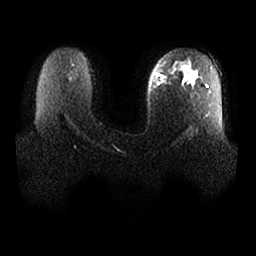
Breast MRI, one axial slice; position 19 of 25 along the scan axis; diffusion-weighted series; image 2 of 4 stored at this slice position (different b-values; order by instance number); 1.5 T; 4 mm slice thickness; 256 × 256 image matrix, field of view 380 × 380 mm. Female patient.
Annotated regions visible in this slice (outlined manually by an expert reader):
- tumour on diffusion-weighted imaging: bounding box [x1, y1, x2, y2] px = [161, 72, 169, 80]